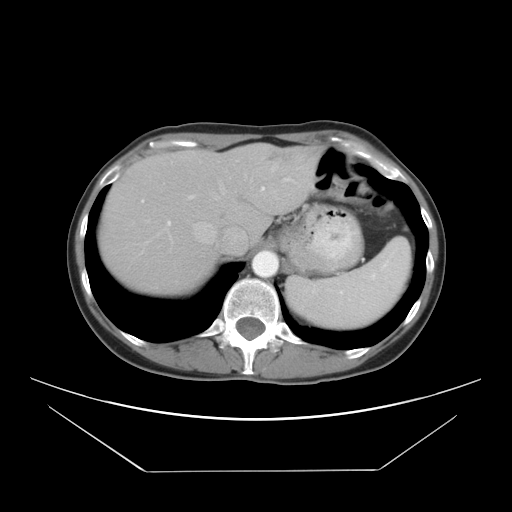
Contrast-enhanced abdominal CT, one axial slice. Position 23 of 30 along the scan axis. Reconstruction kernel STANDARD. Intravenous contrast given. Soft-tissue window (W 400 / L 40 HU). 512 × 512 image matrix. Female patient, age 54 years. Case-level facts recorded for this patient, not image findings: diagnosis: colorectal cancer liver metastases, imaged before liver resection; multiple liver metastases: yes.
Annotated regions visible in this slice (expert manual segmentation):
- hepatic veins: bounding box [x1, y1, x2, y2] px = [138, 165, 278, 256]
- liver: [100, 145, 318, 291]
- planned liver remnant (the part of the liver to remain after resection): [100, 149, 272, 291]
- portal vein (with intrahepatic branches): [143, 186, 265, 246]
- liver metastasis: [267, 155, 277, 163]